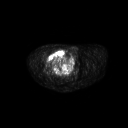
FDG PET of an extremity soft-tissue mass (from a PET/CT study), one axial slice; 3.27 mm slice thickness; 128 × 128 image matrix, field of view 700 × 700 mm. Male patient, age 50 years. Case-level facts recorded for this patient, not image findings: histological type: undifferentiated - pleiomorphic; grade: high; site of the primary tumour: right thigh.
Outlined on this slice (expert contour drawn on MRI and transferred to this co-registered scan by the dataset authors):
- gross tumour volume including surrounding oedema: bounding box [x1, y1, x2, y2] px = [46, 48, 66, 68]
- gross tumour volume (mass): [46, 48, 66, 68]